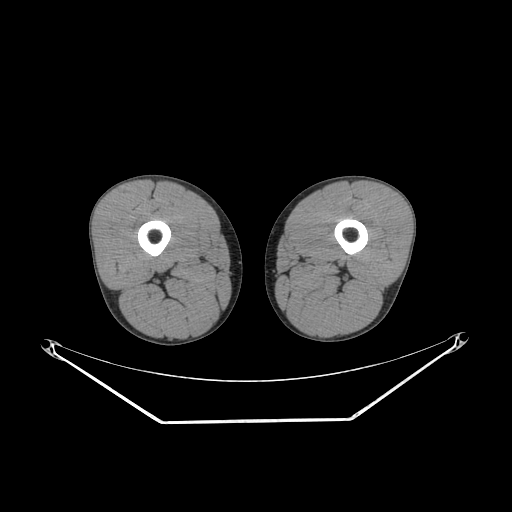
CT of an extremity soft-tissue mass (from a PET/CT study), one axial slice; slice 211 of 267 in the series (ordered by position); reconstruction kernel SOFT; 140 kVp; soft-tissue window (W 400 / L 40 HU); 512 × 512 image matrix, field of view 500 × 500 mm. Male patient. Case-level facts recorded for this patient, not image findings: histological type: extraskeletal osteosarcoma; grade: high; site of the primary tumour: left adductur.
Outlined on this slice (expert contour drawn on MRI and transferred to this co-registered scan by the dataset authors):
- gross tumour volume (mass): bounding box <331,256,348,268> (left, top, right, bottom; pixels)